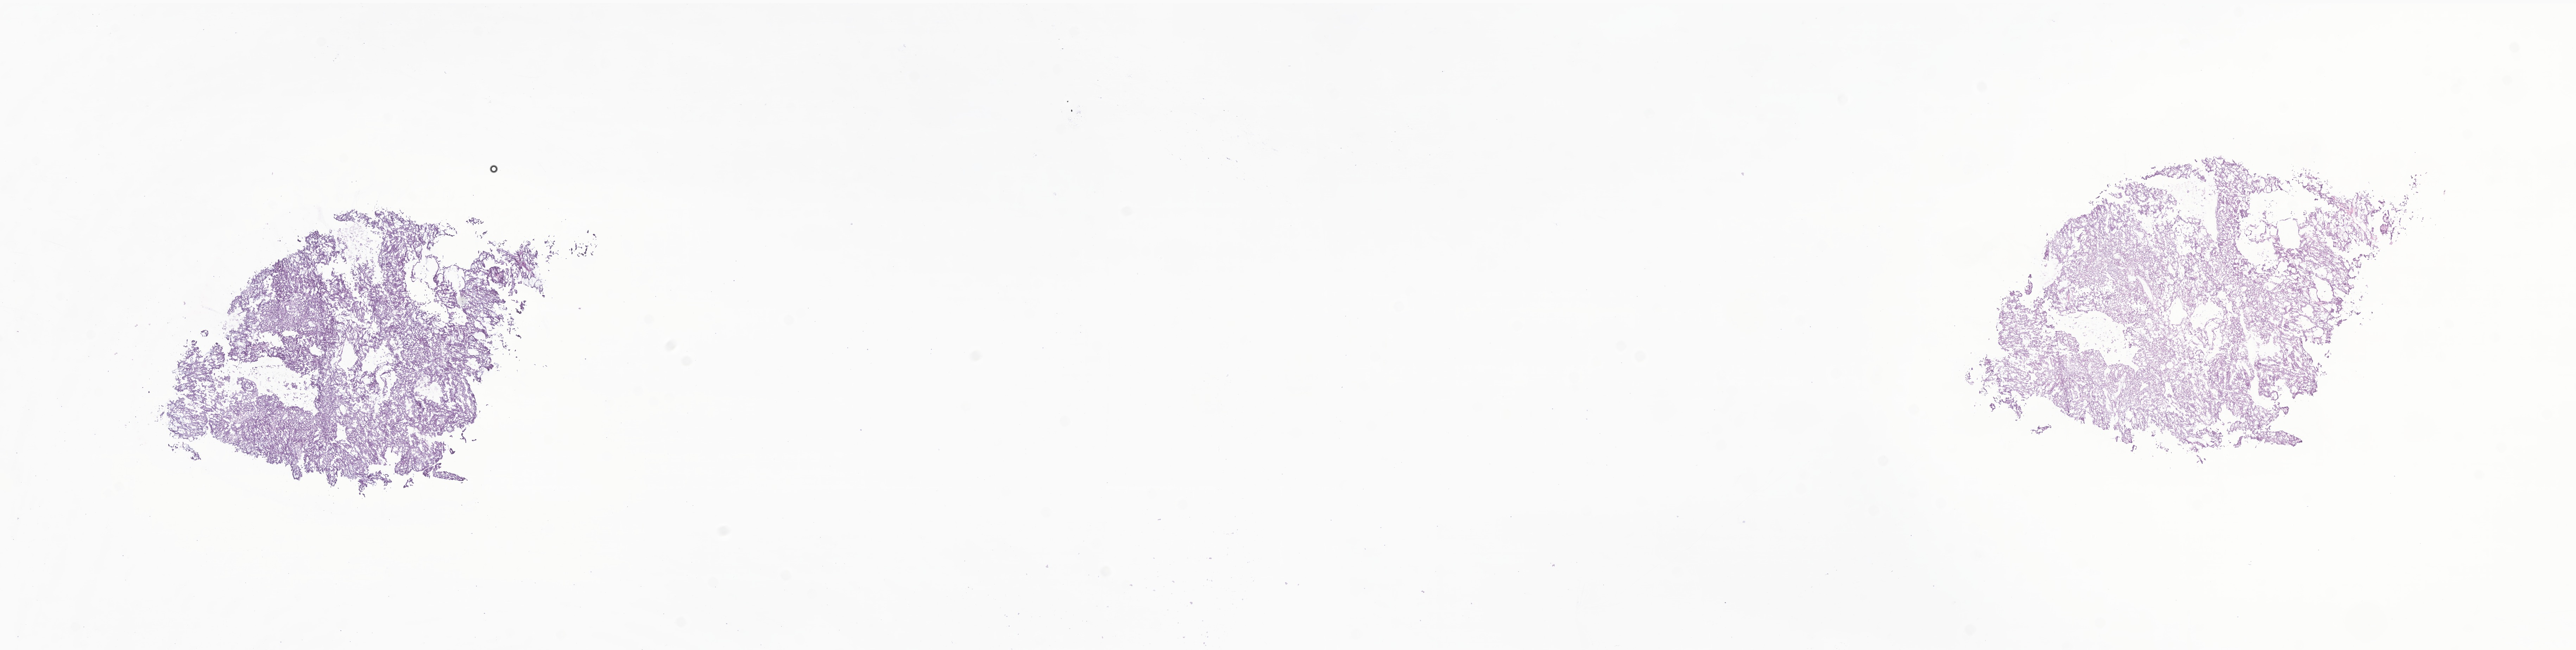
Whole-slide image, haematoxylin and eosin stain of tumor tissue from the pancreas, a low-resolution overview of the entire scanned area, about 30.9 x 7.8 mm; frozen section. Patient female; age 183 months (15 years 3 months).
Diagnosis (ICD-O-3 morphology term): Solid pseudopapillary tumor of ovary.